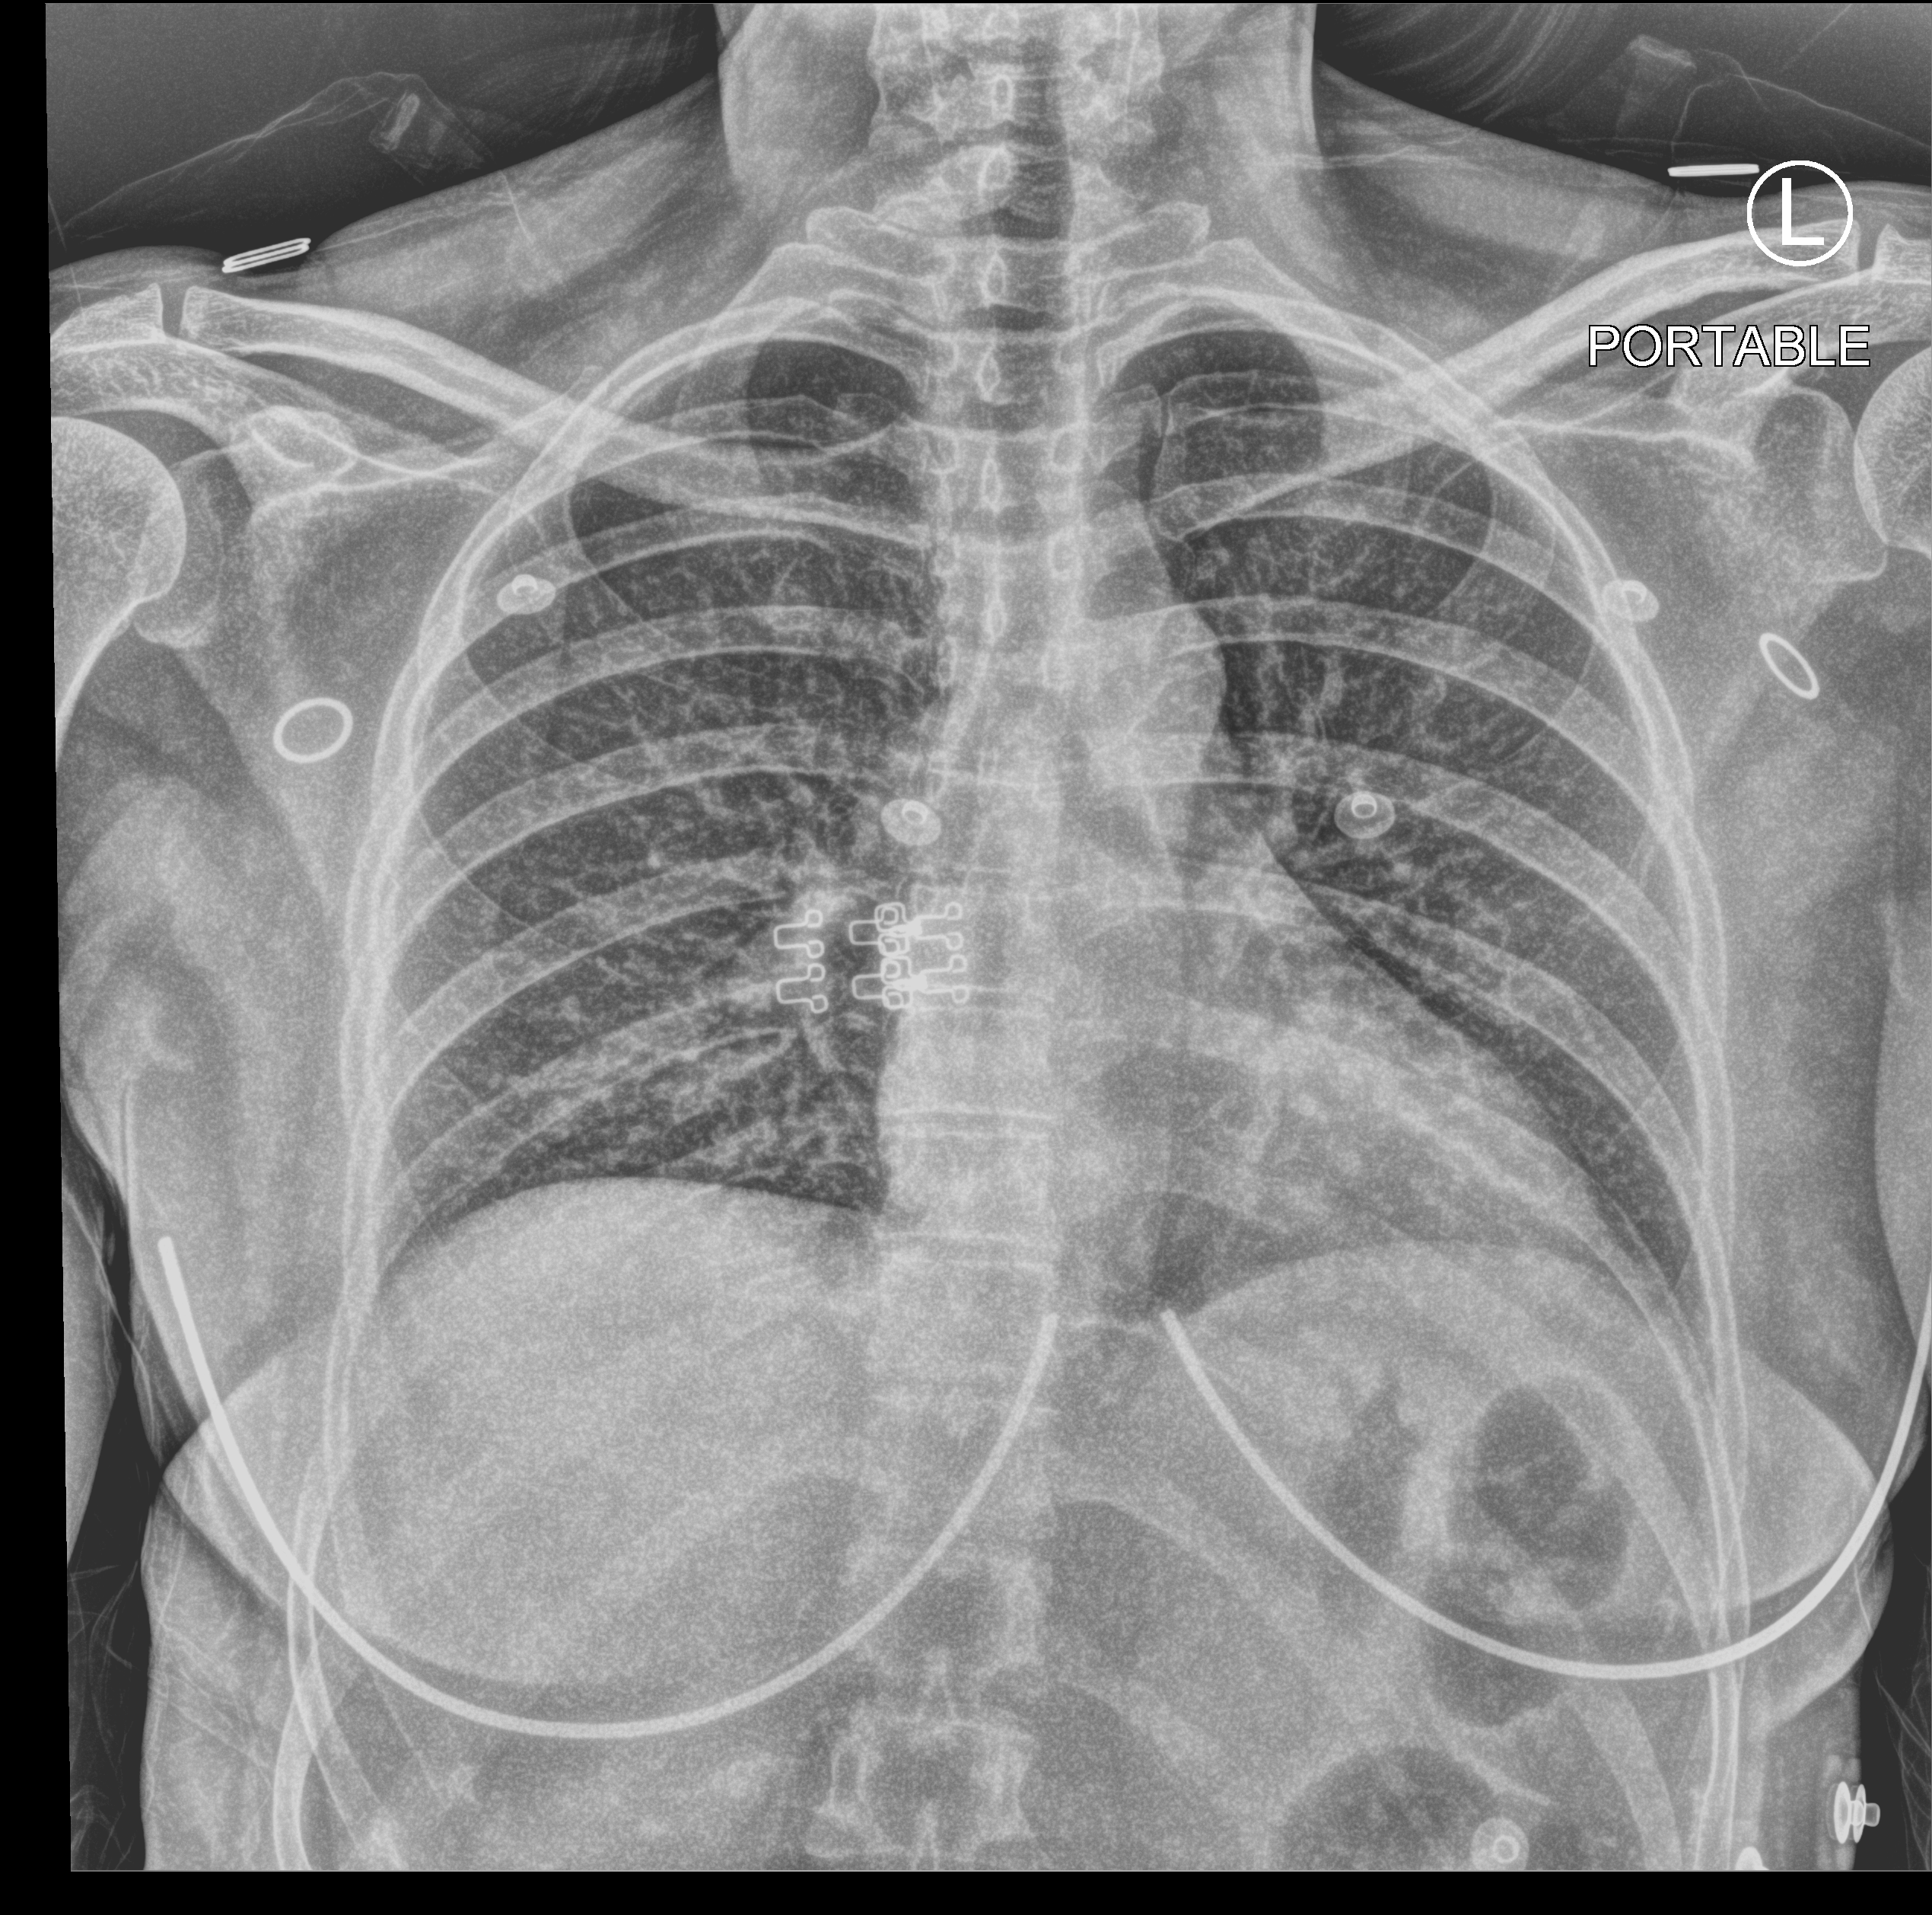
Chest X-ray (portable); anteroposterior (AP) projection. Female patient hospitalised with COVID-19, age 18–59 years.
Hospital-stay facts (about this admission, not read from this image; timing relative to this image not recorded): mechanically ventilated during this hospital stay: no; diabetes (admission record): no.